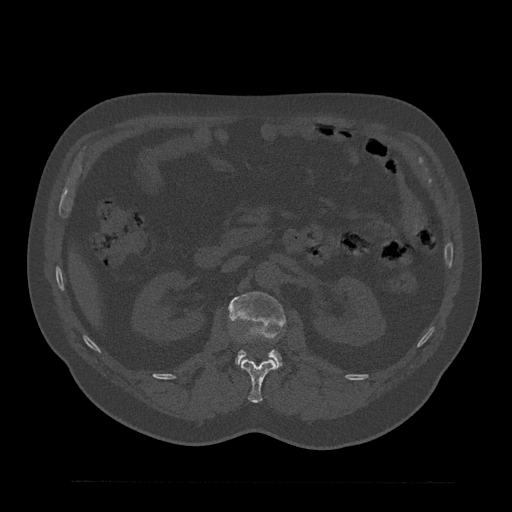
CT including the spine, one axial slice; slice 134 of 797 in the series (ordered by position); reconstruction kernel Br40s/3; 120 kVp; bone window (W 1800 / L 400 HU); 0.5 mm slice thickness; 512 × 512 image matrix, field of view 430 × 430 mm. Male patient, age 61 years. From the clinical record (not read from this slice): primary cancer: prostate.
Structures marked on this image (semi-automatically segmented with operator editing):
- L1 vertebra: box from (x=240, y=359) to (x=277, y=403) px
- L2 vertebra: (x=229, y=292)–(x=285, y=367)